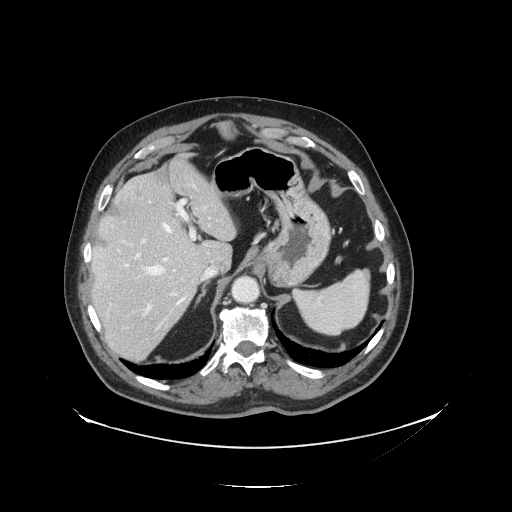
Contrast-enhanced abdominal CT, one axial slice. Slice 99 of 138 in the series (ordered by position). 120 kVp. Soft-tissue window (W 400 / L 40 HU). 2.5 mm slice thickness. 512 × 512 image matrix, field of view 497 × 497 mm. Male patient, age 77 years. Case-level facts recorded for this patient, not image findings: diagnosis: colorectal cancer liver metastases, imaged before liver resection; multiple liver metastases: no; largest metastasis: 1.5 cm; disease in both lobes: no.
Annotated regions visible in this slice (outlined manually by an expert reader):
- hepatic veins: bounding box <142,217,211,306> (left, top, right, bottom; pixels)
- liver: <92,159,235,361>
- planned liver remnant (the part of the liver to remain after resection): <92,159,235,288>
- portal vein (with intrahepatic branches): <135,200,210,316>